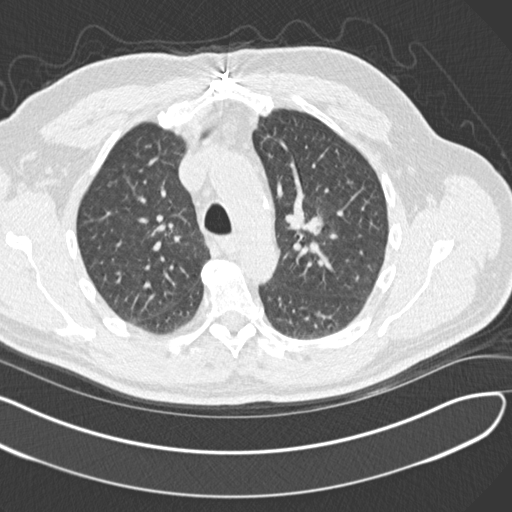
Low-dose screening chest CT, axial slice, second screening round (one year after baseline), lung window (W 1500 / L -600 HU), 2 mm slice thickness, standard (soft-tissue) reconstruction kernel (B30f). Male, age 65 years at enrolment. Former smoker at enrolment.
Expert-annotated lung lesion, bounding box (x1, y1, x2, y2) in pixels: (284, 197, 339, 258). The screening reader recorded 4 non-calcified nodules or masses ≥4 mm on this exam (left upper lobe, left upper lobe, left lower lobe, right middle lobe); which of them this box marks is not recorded. Official screen result: positive, other. Later outcome: lung cancer diagnosed 577 days after this screen — acinar cell carcinoma, left upper lobe, stage IA (AJCC 6th edition), 25 mm at pathology.